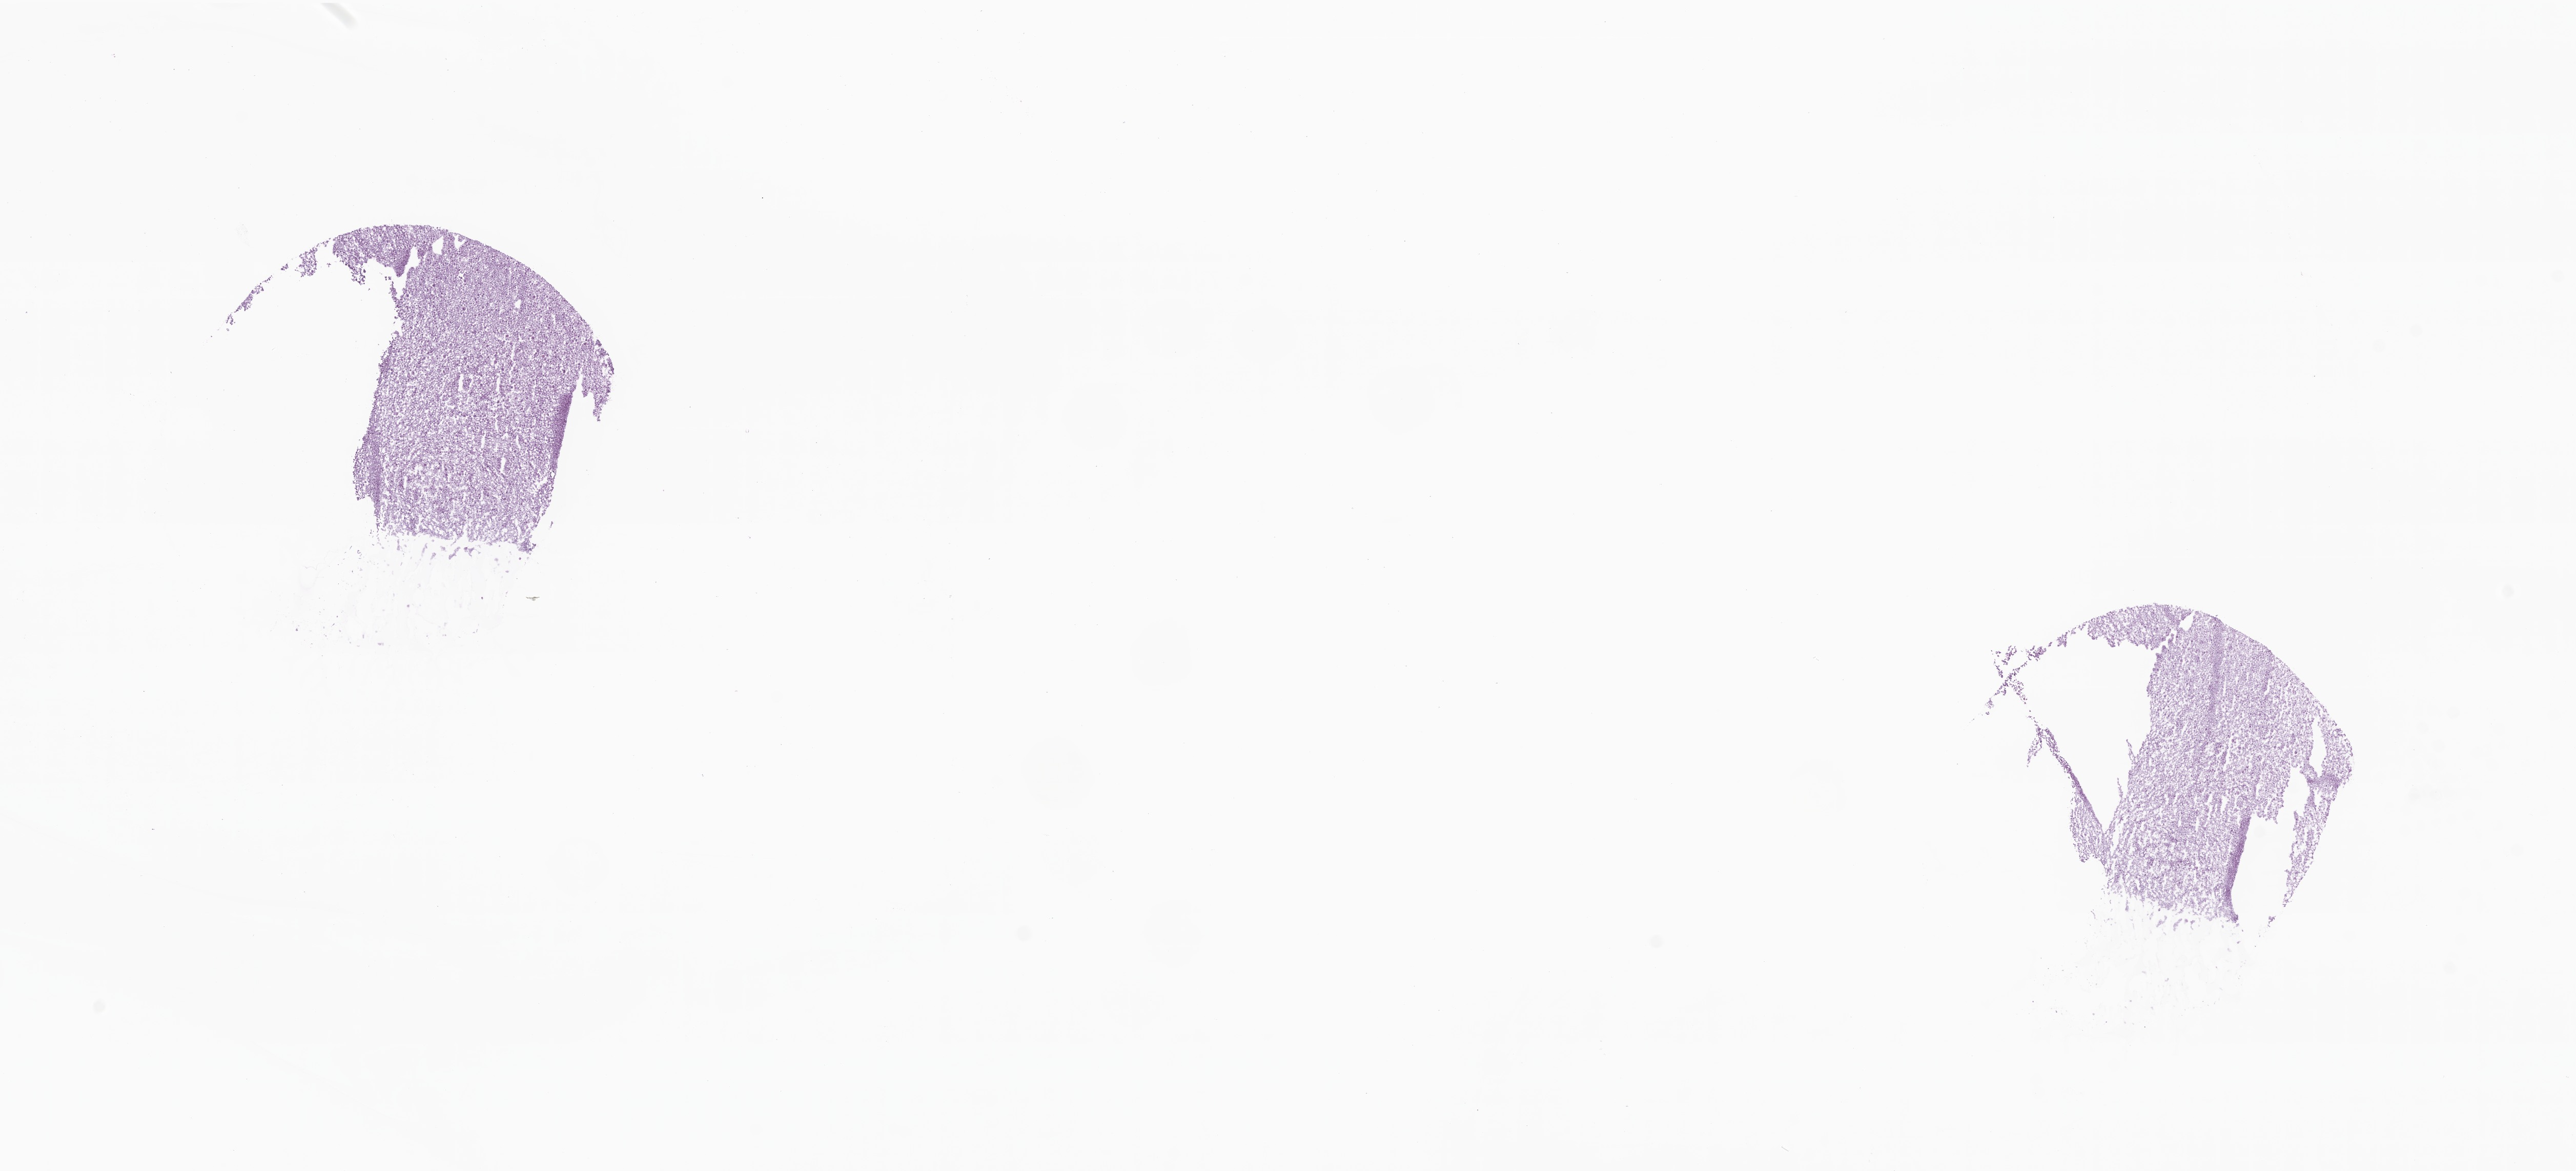
Haematoxylin and eosin whole-slide image — a low-resolution overview of the entire scanned area, about 21.2 x 9.6 mm, frozen section, metastatic tumor tissue. Female, age 50 years at initial diagnosis. Pathologist review of this section (percent, as recorded): tumor cells 95%, tumor nuclei 95%, stromal cells 5%, necrosis 0%, normal cells 0%. Infiltration values recorded for this section: lymphocyte infiltration 0%, monocyte infiltration 0%, neutrophil infiltration 0%.
Patient diagnosis (primary): Adenocarcinoma, metastatic, NOS.